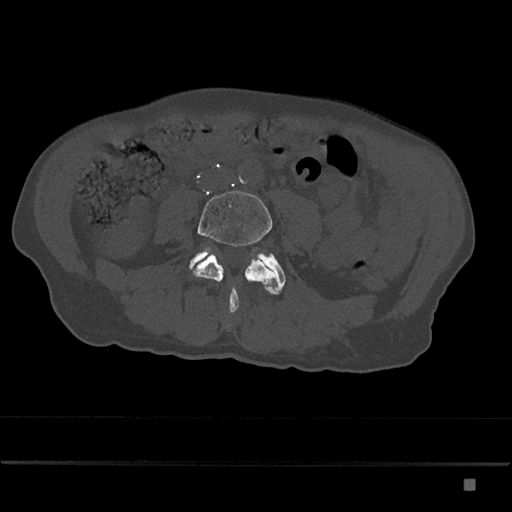
CT including the spine, one axial slice; position 323 of 797 along the scan axis; bone window (W 1800 / L 400 HU); 0.5 mm slice thickness; 512 × 512 image matrix, field of view 390 × 390 mm. Patient: male, 72 years. Case-level facts recorded for this patient, not image findings: primary cancer: prostate.
Structures marked on this image (semi-automatically segmented with operator editing):
- L4 vertebra: bounding box [x1, y1, x2, y2] px = [189, 190, 277, 313]
- L5 vertebra: [189, 247, 286, 294]